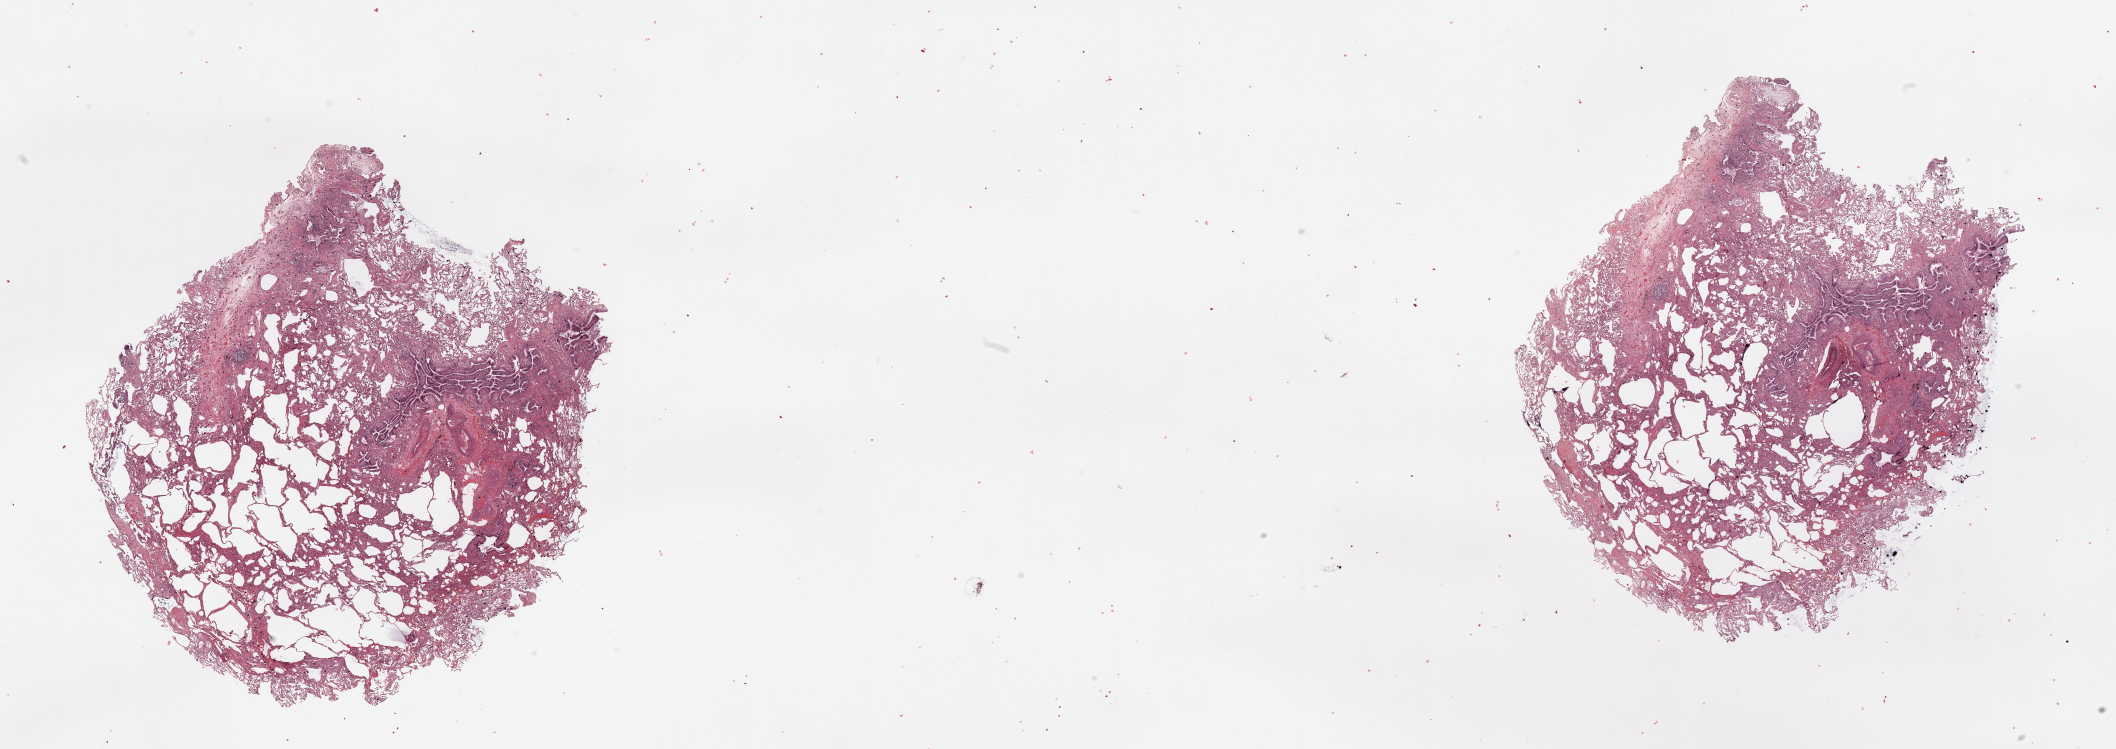
Whole-slide histology image, Hematoxylin and eosin (H&E) stained, low-resolution overview of the scanned area, about 33.5 x 11.8 mm. Normal (non-tumour) tissue sample, lung. 68-year-old male patient.
This section: normal (non-tumour) tissue from the same patient. Patient diagnosis (cohort enrolment): squamous cell carcinoma (lung).